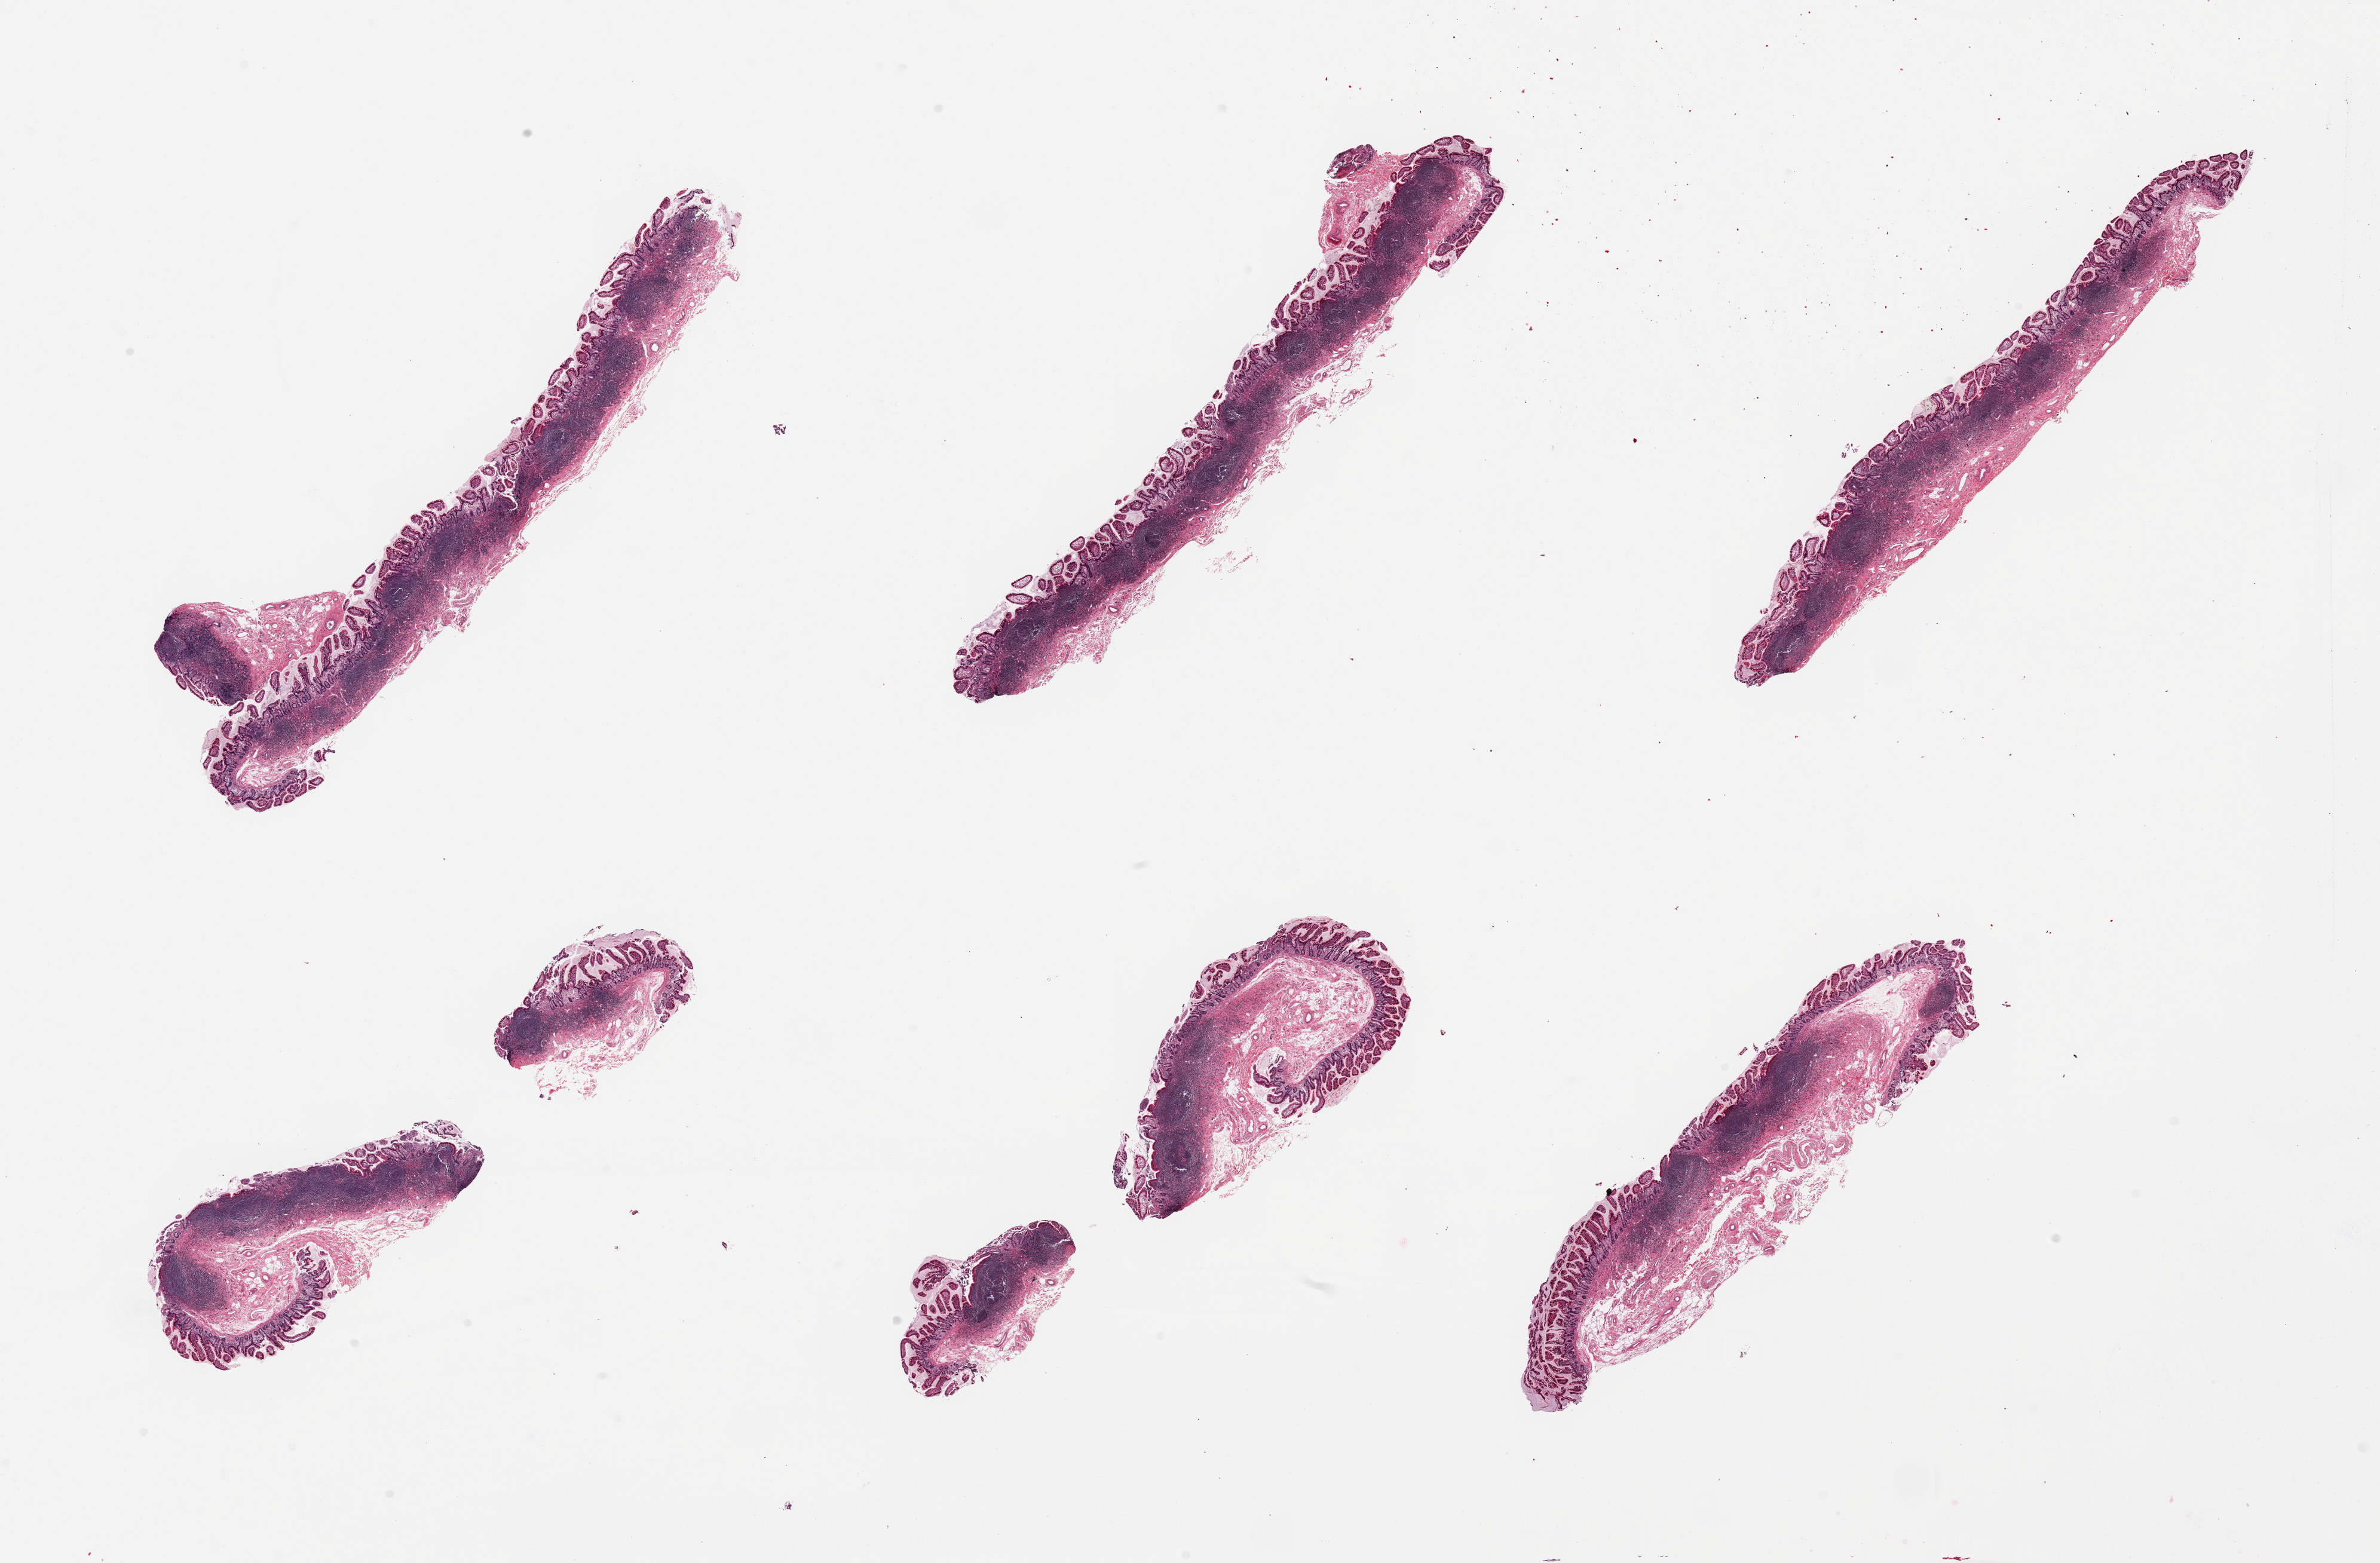
Whole-slide image, hematoxylin and eosin (H&E) stain, a low-resolution overview of the entire scanned area, about 31.5 x 20.7 mm. PAXgene-fixed paraffin-embedded (PFPE) section. Sampled site (target tissue): ileum. Tissue donor sample. Female donor.
Review note (as recorded): 6 pieces, all mucosa, well preserved, abudnant lymphoid/Peyer aggregates are ~50% of tissue.